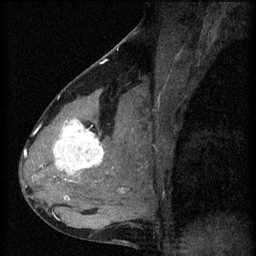
Breast MRI (dynamic contrast-enhanced), one sagittal slice. Slice 36 of 60 in the series (ordered by position). 3 images stored at this slice position (order not interpretable as contrast timing). 1.5 T. TE 4.2 ms, TR 8.2 ms. 2 mm slice thickness. 256 × 256 image matrix. Female patient, age 37 years.
Outlined on this slice (semi-automatically segmented with operator editing):
- analysis volume of interest (the breast-tissue region the enhancement analysis was run in; not a lesion): box from (x=44, y=100) to (x=119, y=197) px
- tumour enhancement mask (voxels above the 70 % enhancement threshold inside the analysis volume of interest): (x=54, y=118)–(x=105, y=197)